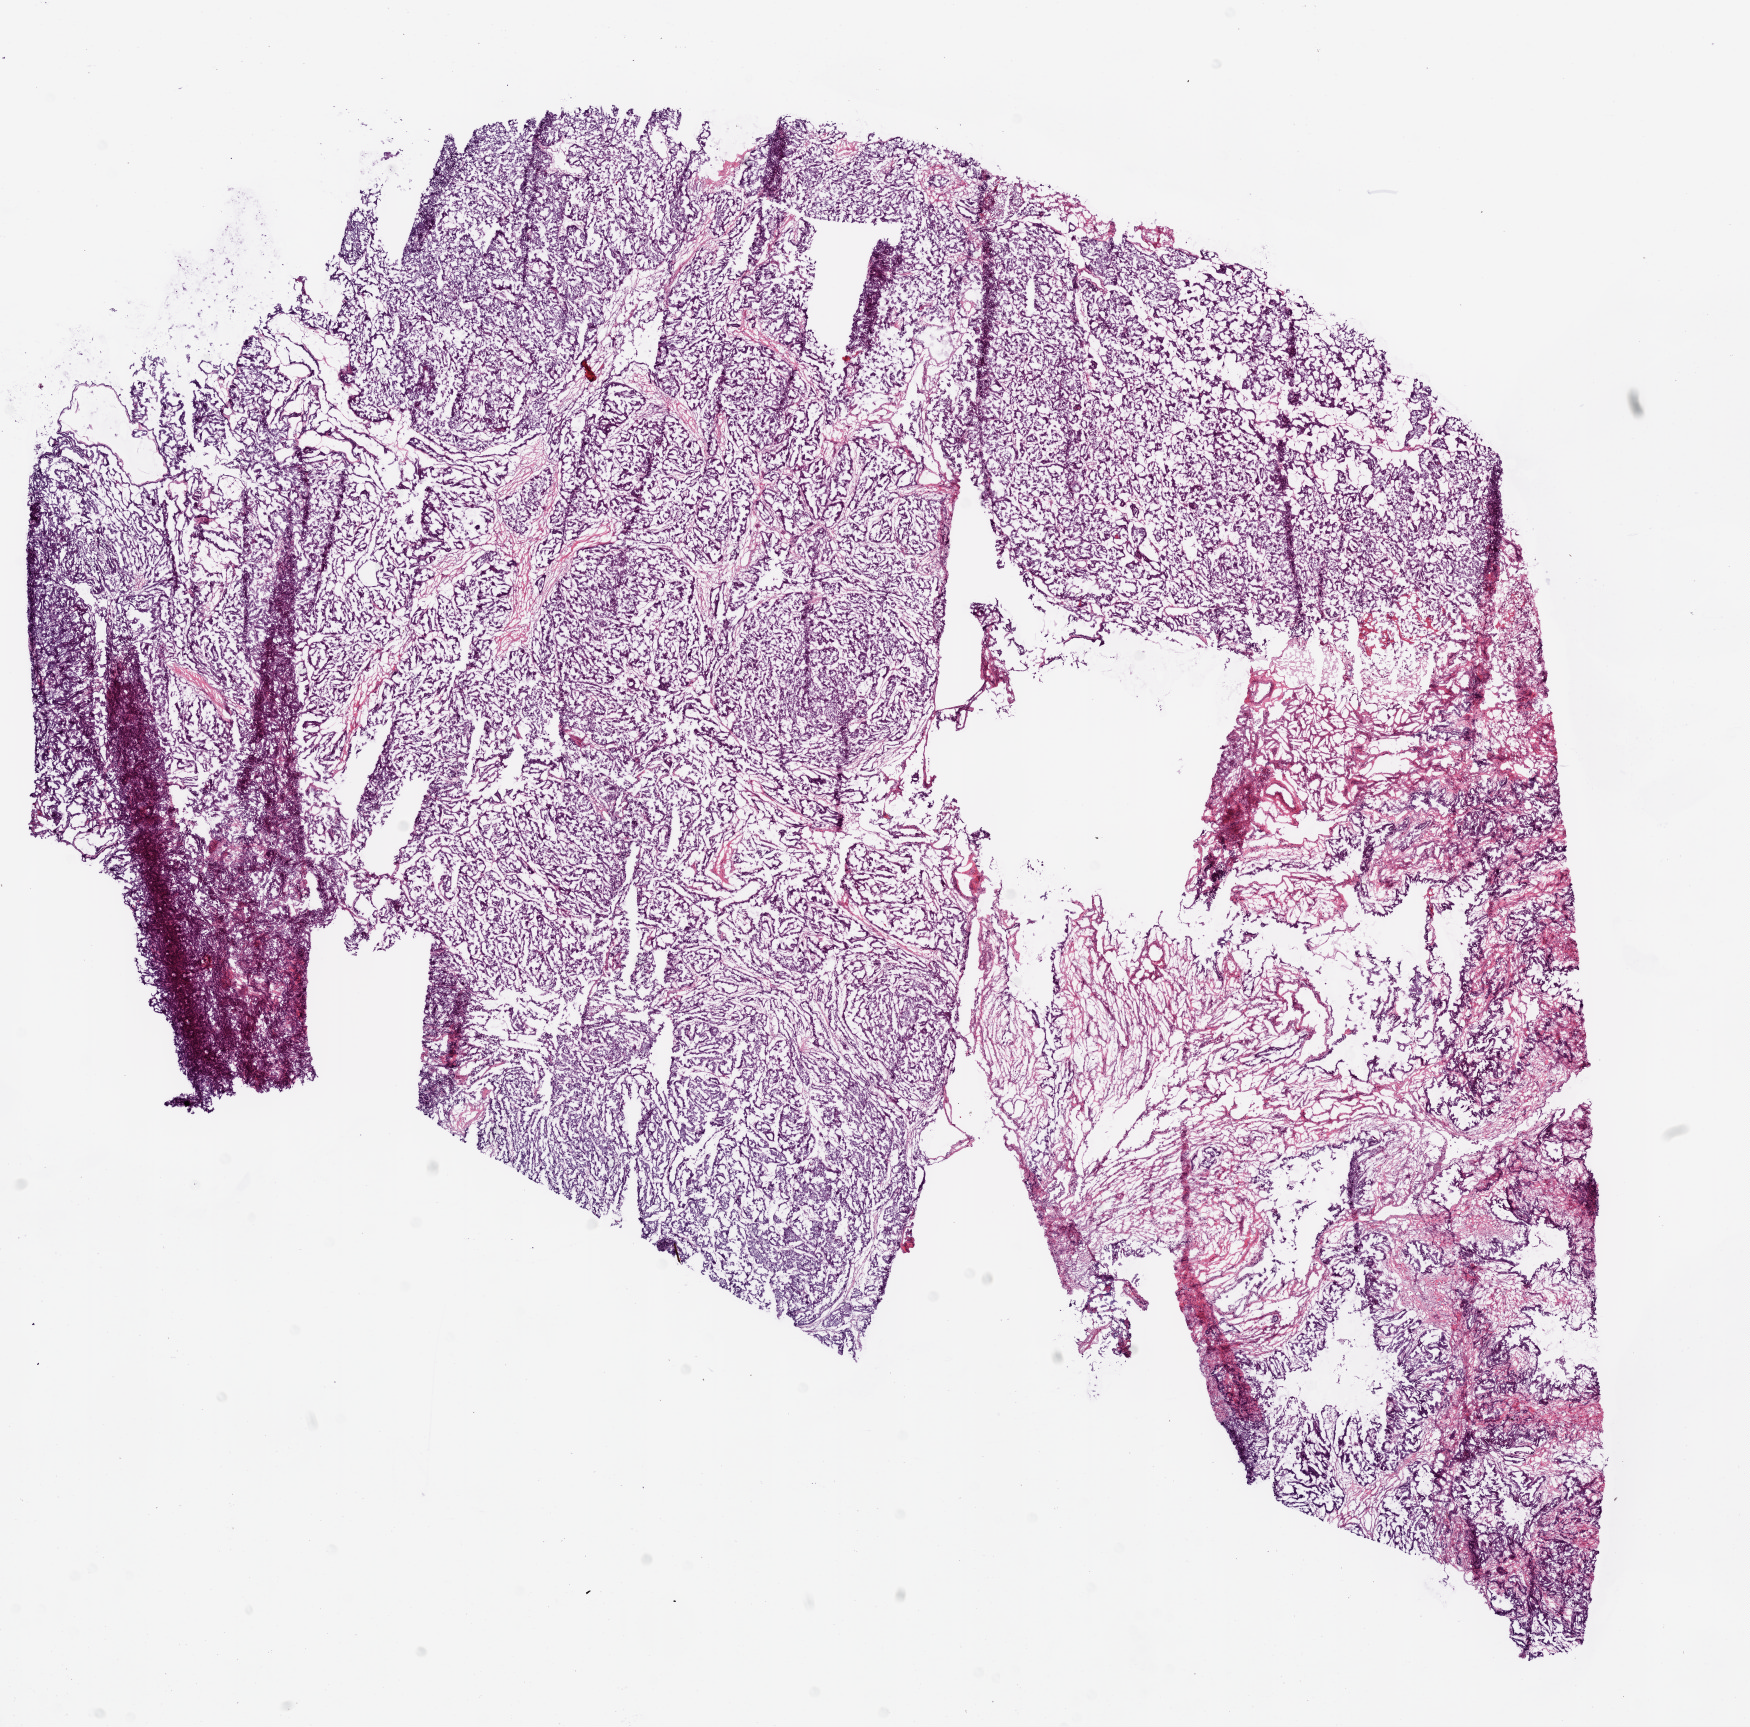
H&E whole-slide image, a low-resolution overview of the entire scanned area, about 14.0 x 13.9 mm, frozen section, ovary, primary tumour sample. Female patient; age at initial diagnosis 50 years. Histologic grade: G3 (poorly differentiated). Composition of this section per pathologist review: tumour cells 95%, tumour nuclei 85%, normal cells 0%, stromal cells 5%, necrosis 0%.
• FIGO stage: IIB
• histologic diagnosis: Serous cystadenocarcinoma, NOS
• laterality: left